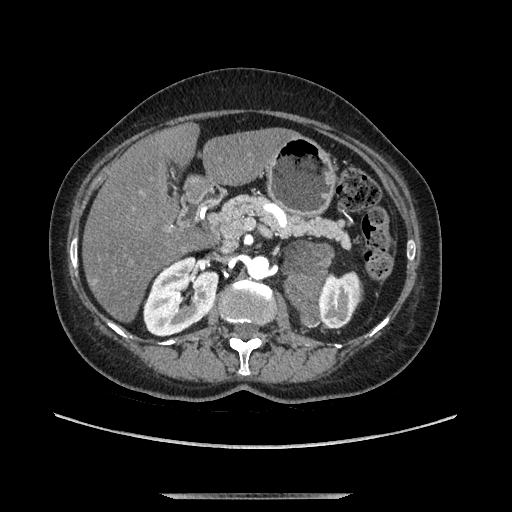
Contrast-enhanced abdominal CT, one axial slice. Position 62 of 169 along the scan axis. Soft-tissue window (W 400 / L 40 HU). 1.25 mm slice thickness. 512 × 512 image matrix. Female patient. Case-level facts recorded for this patient, not image findings: diagnosis: adrenocortical carcinoma; tumour side: left adrenal; tumour size at pathology: 9 cm; Ki-67 index: 2 %; stage (as recorded): 3.
Outlined on this slice (semi-automatically segmented with operator editing):
- mass: bounding box (x1, y1, x2, y2) in pixels: (284, 241, 331, 324)